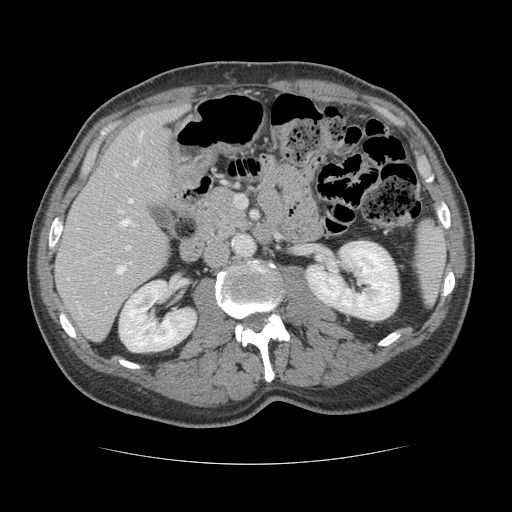
Contrast-enhanced abdominal CT, one axial slice; slice 61 of 134 in the series (ordered by position); intravenous contrast given; soft-tissue window (W 400 / L 40 HU); 2.5 mm slice thickness; 512 × 512 image matrix, field of view 377 × 377 mm. Male patient, age 68 years. From the clinical record (not read from this slice): diagnosis: colorectal cancer liver metastases, imaged before liver resection; multiple liver metastases: yes; largest metastasis: 2.2 cm; disease in both lobes: no.
Annotated regions visible in this slice (manually delineated by an expert):
- hepatic veins: box from (x=116, y=133) to (x=142, y=226) px
- liver: (x=56, y=110)–(x=178, y=340)
- planned liver remnant (the part of the liver to remain after resection): (x=56, y=110)–(x=178, y=335)
- portal vein (with intrahepatic branches): (x=117, y=210)–(x=131, y=273)